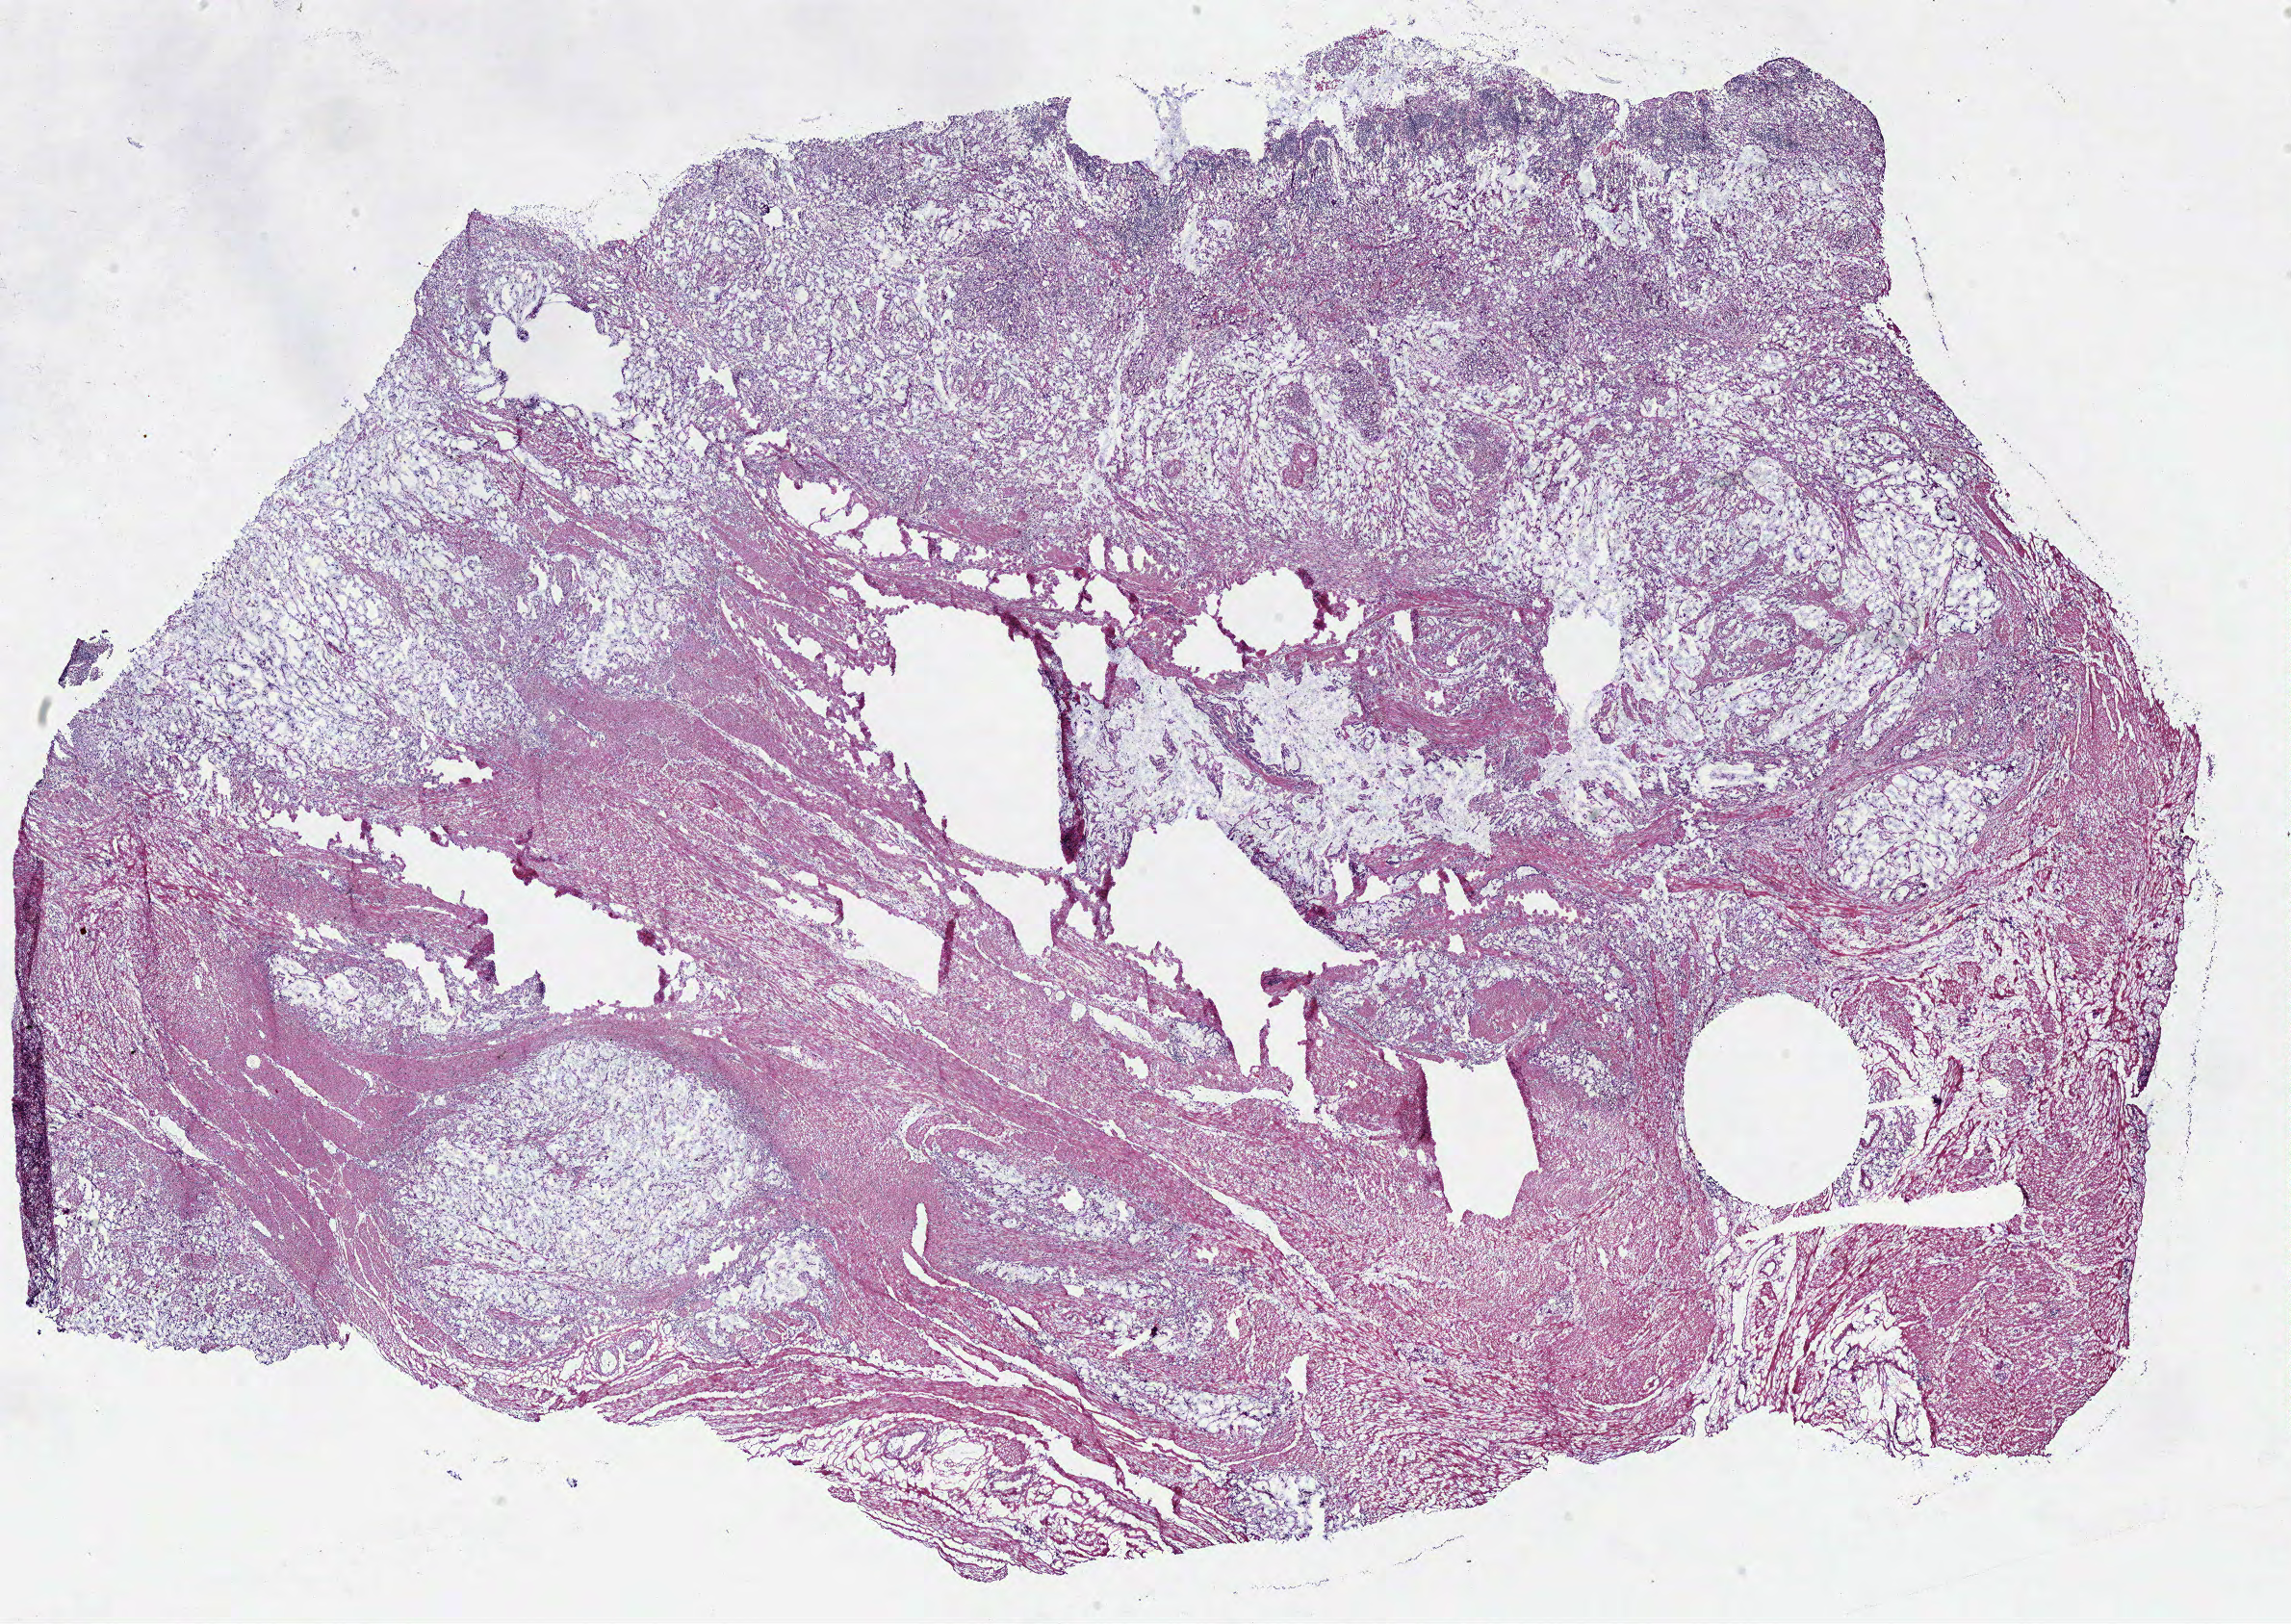
Whole-slide histology image, H&E — whole scanned area (about 18.8 x 13.3 mm, from a 40x scan) shown as a low-resolution overview. Frozen section from the bottom of the tissue portion. Primary tumour sample from the stomach. Male, age 82 years at initial diagnosis. Pathologist review of this section (percent, as recorded): tumour cells 60%, tumour nuclei 65%.
Diagnosis: Mucinous adenocarcinoma (gastric antrum).